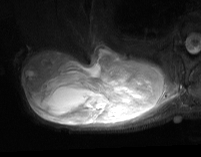
MRI of an extremity soft-tissue mass, one axial slice. Position 36 of 74 along the scan axis. STIR. MR volume resampled by the dataset authors to the PET/CT grid (not the native acquisition matrix). 3.27 mm slice thickness. 201 × 157 image matrix, field of view 196 × 153 mm. Male patient. Case-level facts recorded for this patient, not image findings: histological type: pleiomorphic spindle cell undifferentiated; grade: high; site of the primary tumour: right parascapusular.
Structures marked on this image (expert contour drawn on MRI and transferred to this co-registered scan by the dataset authors):
- gross tumour volume including surrounding oedema: box from (x=21, y=45) to (x=180, y=129) px
- gross tumour volume (mass): (x=23, y=46)–(x=166, y=126)